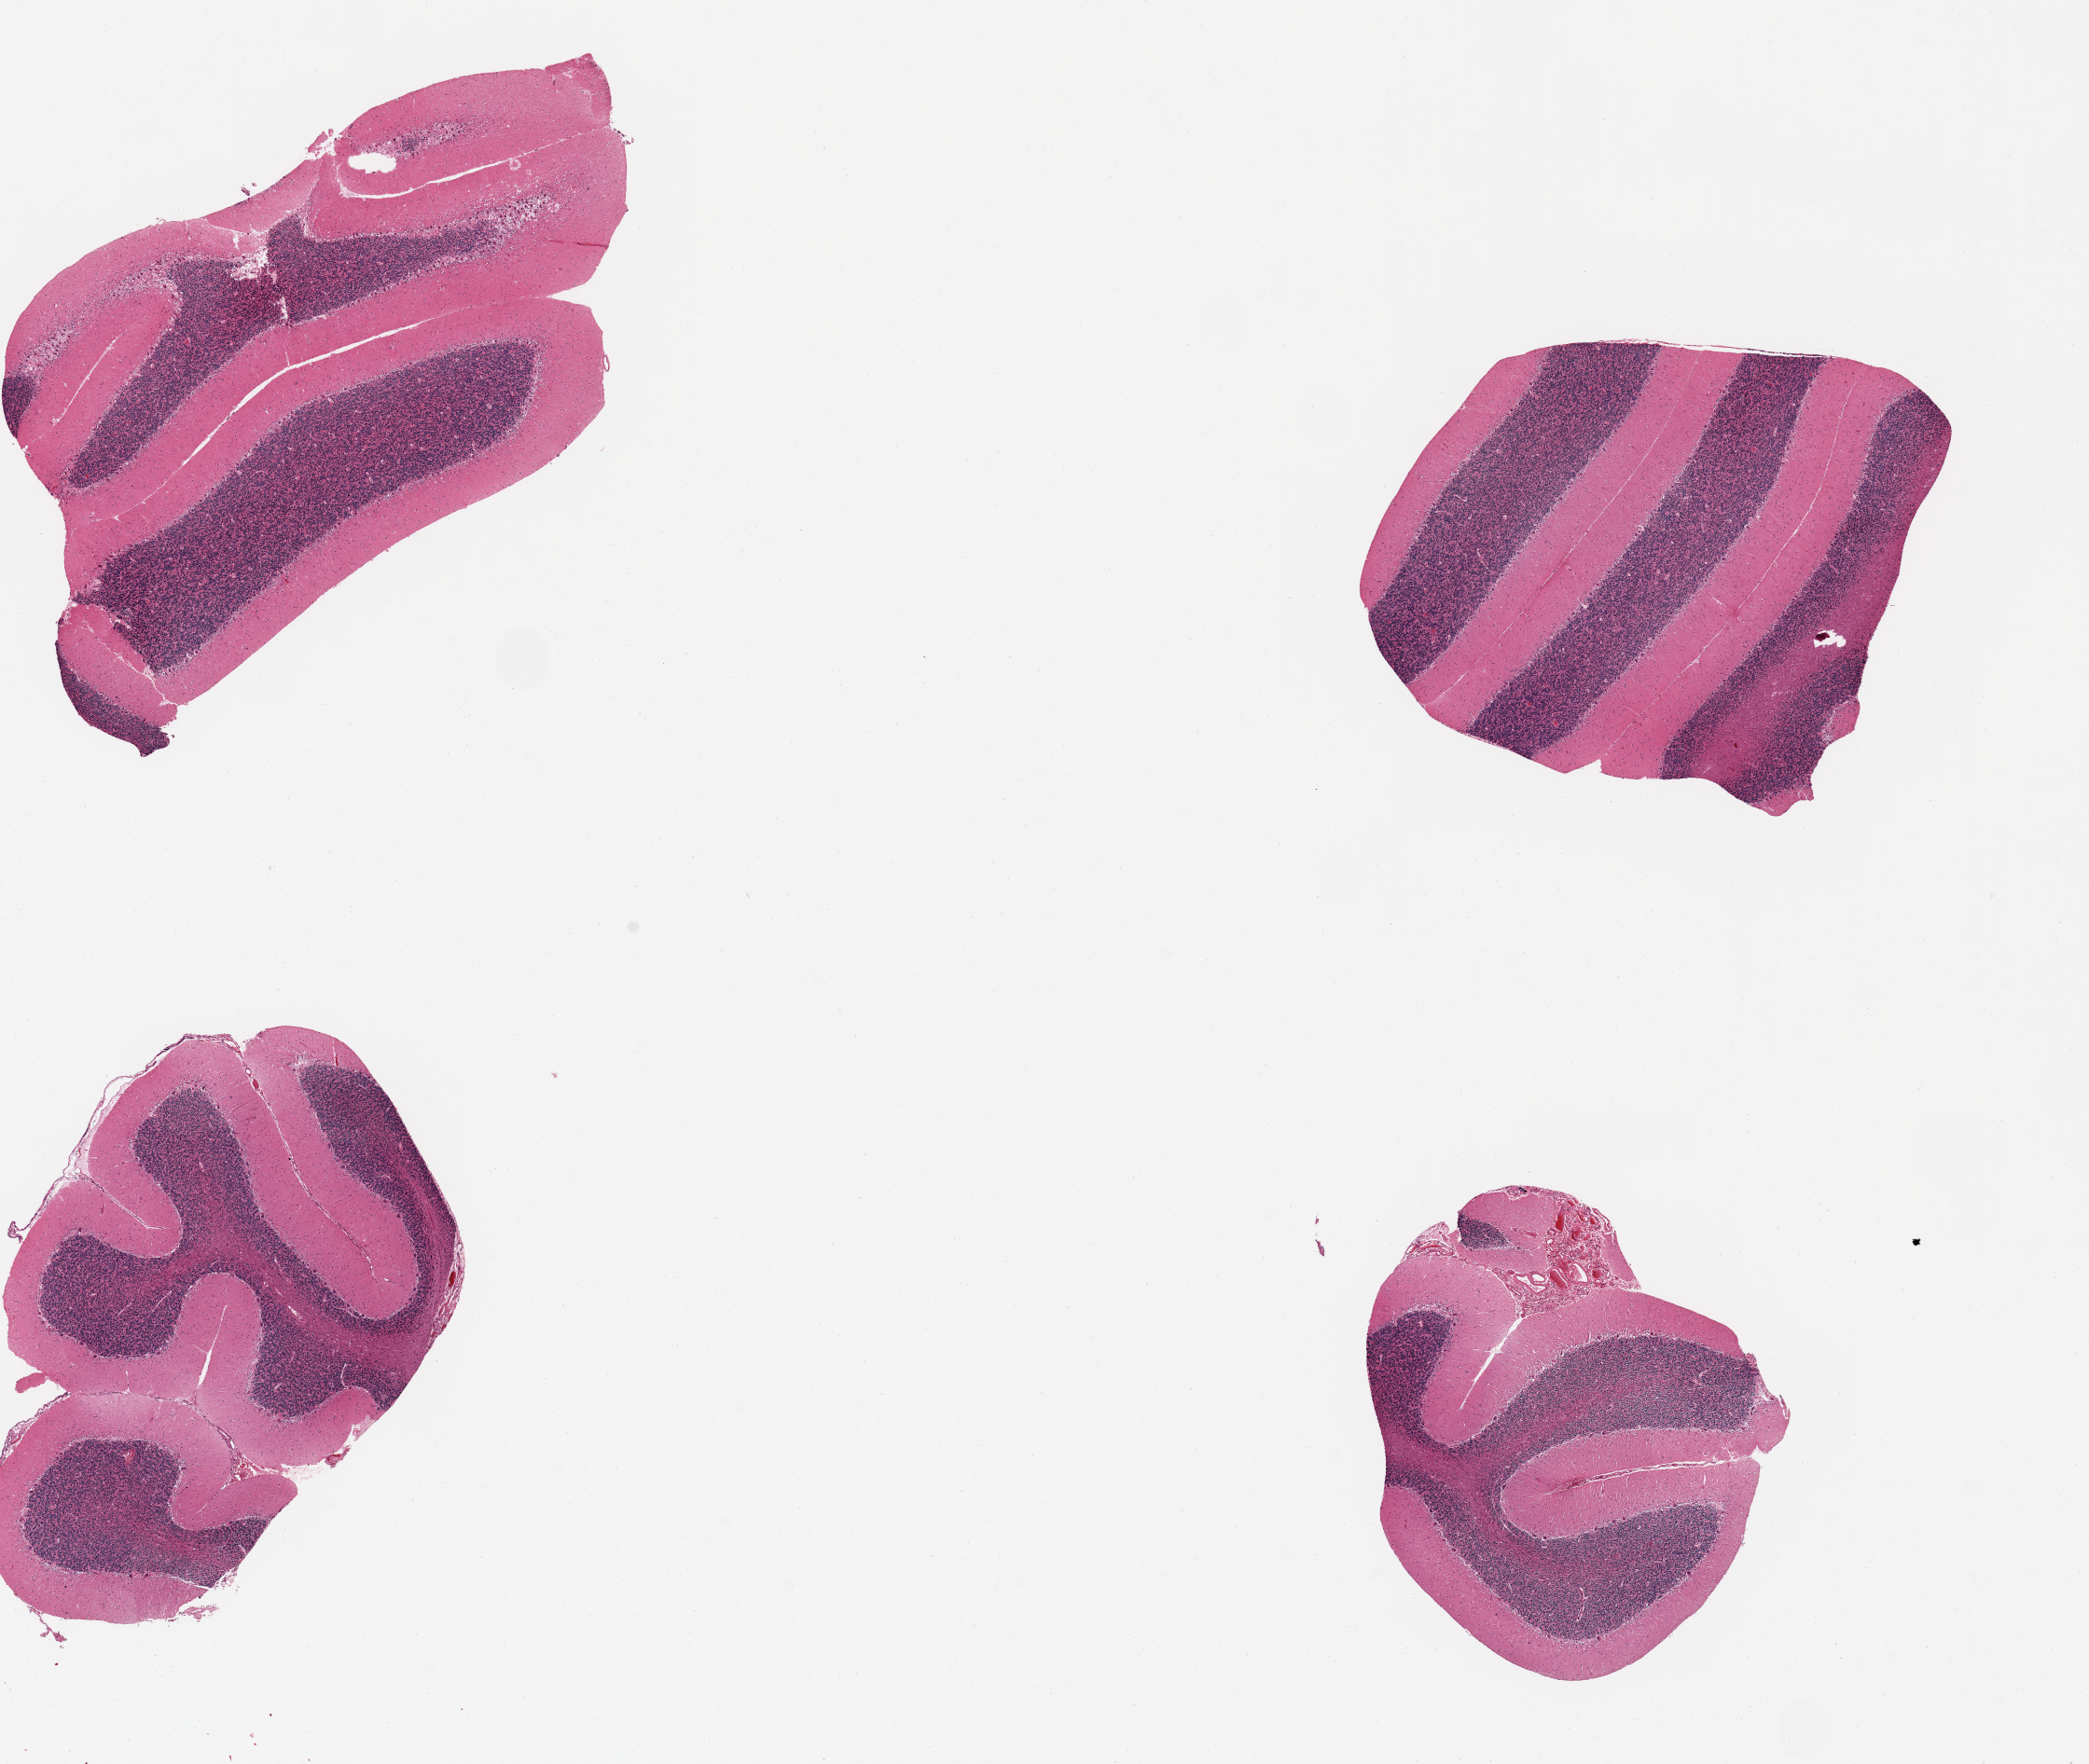
Digitized H&E-stained section — whole scanned area (about 17.7 x 15.0 mm, acquisition: 20x scan) shown as a low-resolution overview. PAXgene-fixed, paraffin-embedded tissue. Section of cerebellum (target tissue). Tissue donor sample. Donor sex: female.
Reviewer comment on this tissue sample: 4 pieces up to 5x3.5 mm.